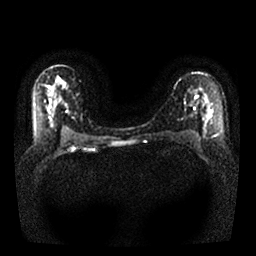
Breast MRI, one axial slice. Position 16 of 25 along the scan axis. Diffusion-weighted series; image 2 of 4 stored at this slice position (different b-values; order by instance number). 1.5 T. 4 mm slice thickness. 256 × 256 image matrix, field of view 340 × 340 mm. Female patient.
Structures marked on this image (expert manual segmentation):
- tumour on diffusion-weighted imaging: bounding box <207,109,213,119> (left, top, right, bottom; pixels)